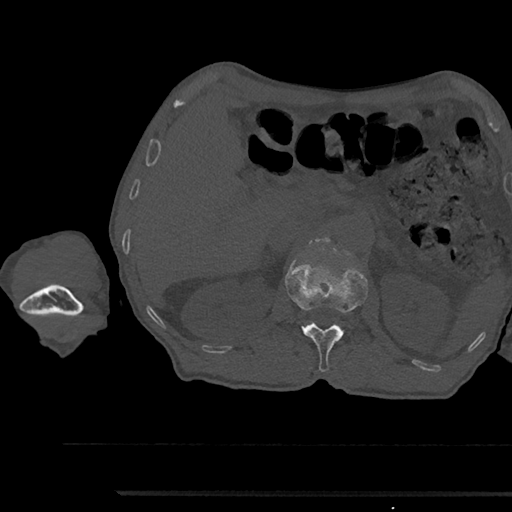
CT including the spine, one axial slice. Position 627 of 797 along the scan axis. Reconstruction kernel Br40s/3. Bone window (W 1800 / L 400 HU). 512 × 512 image matrix. Patient: male, 79 years. Case-level facts recorded for this patient, not image findings: primary cancer: prostate.
Annotated regions visible in this slice (semi-automatically segmented with operator editing):
- L1 vertebra: box from (x=285, y=261) to (x=368, y=372) px
- L2 vertebra: (x=314, y=238)–(x=328, y=242)